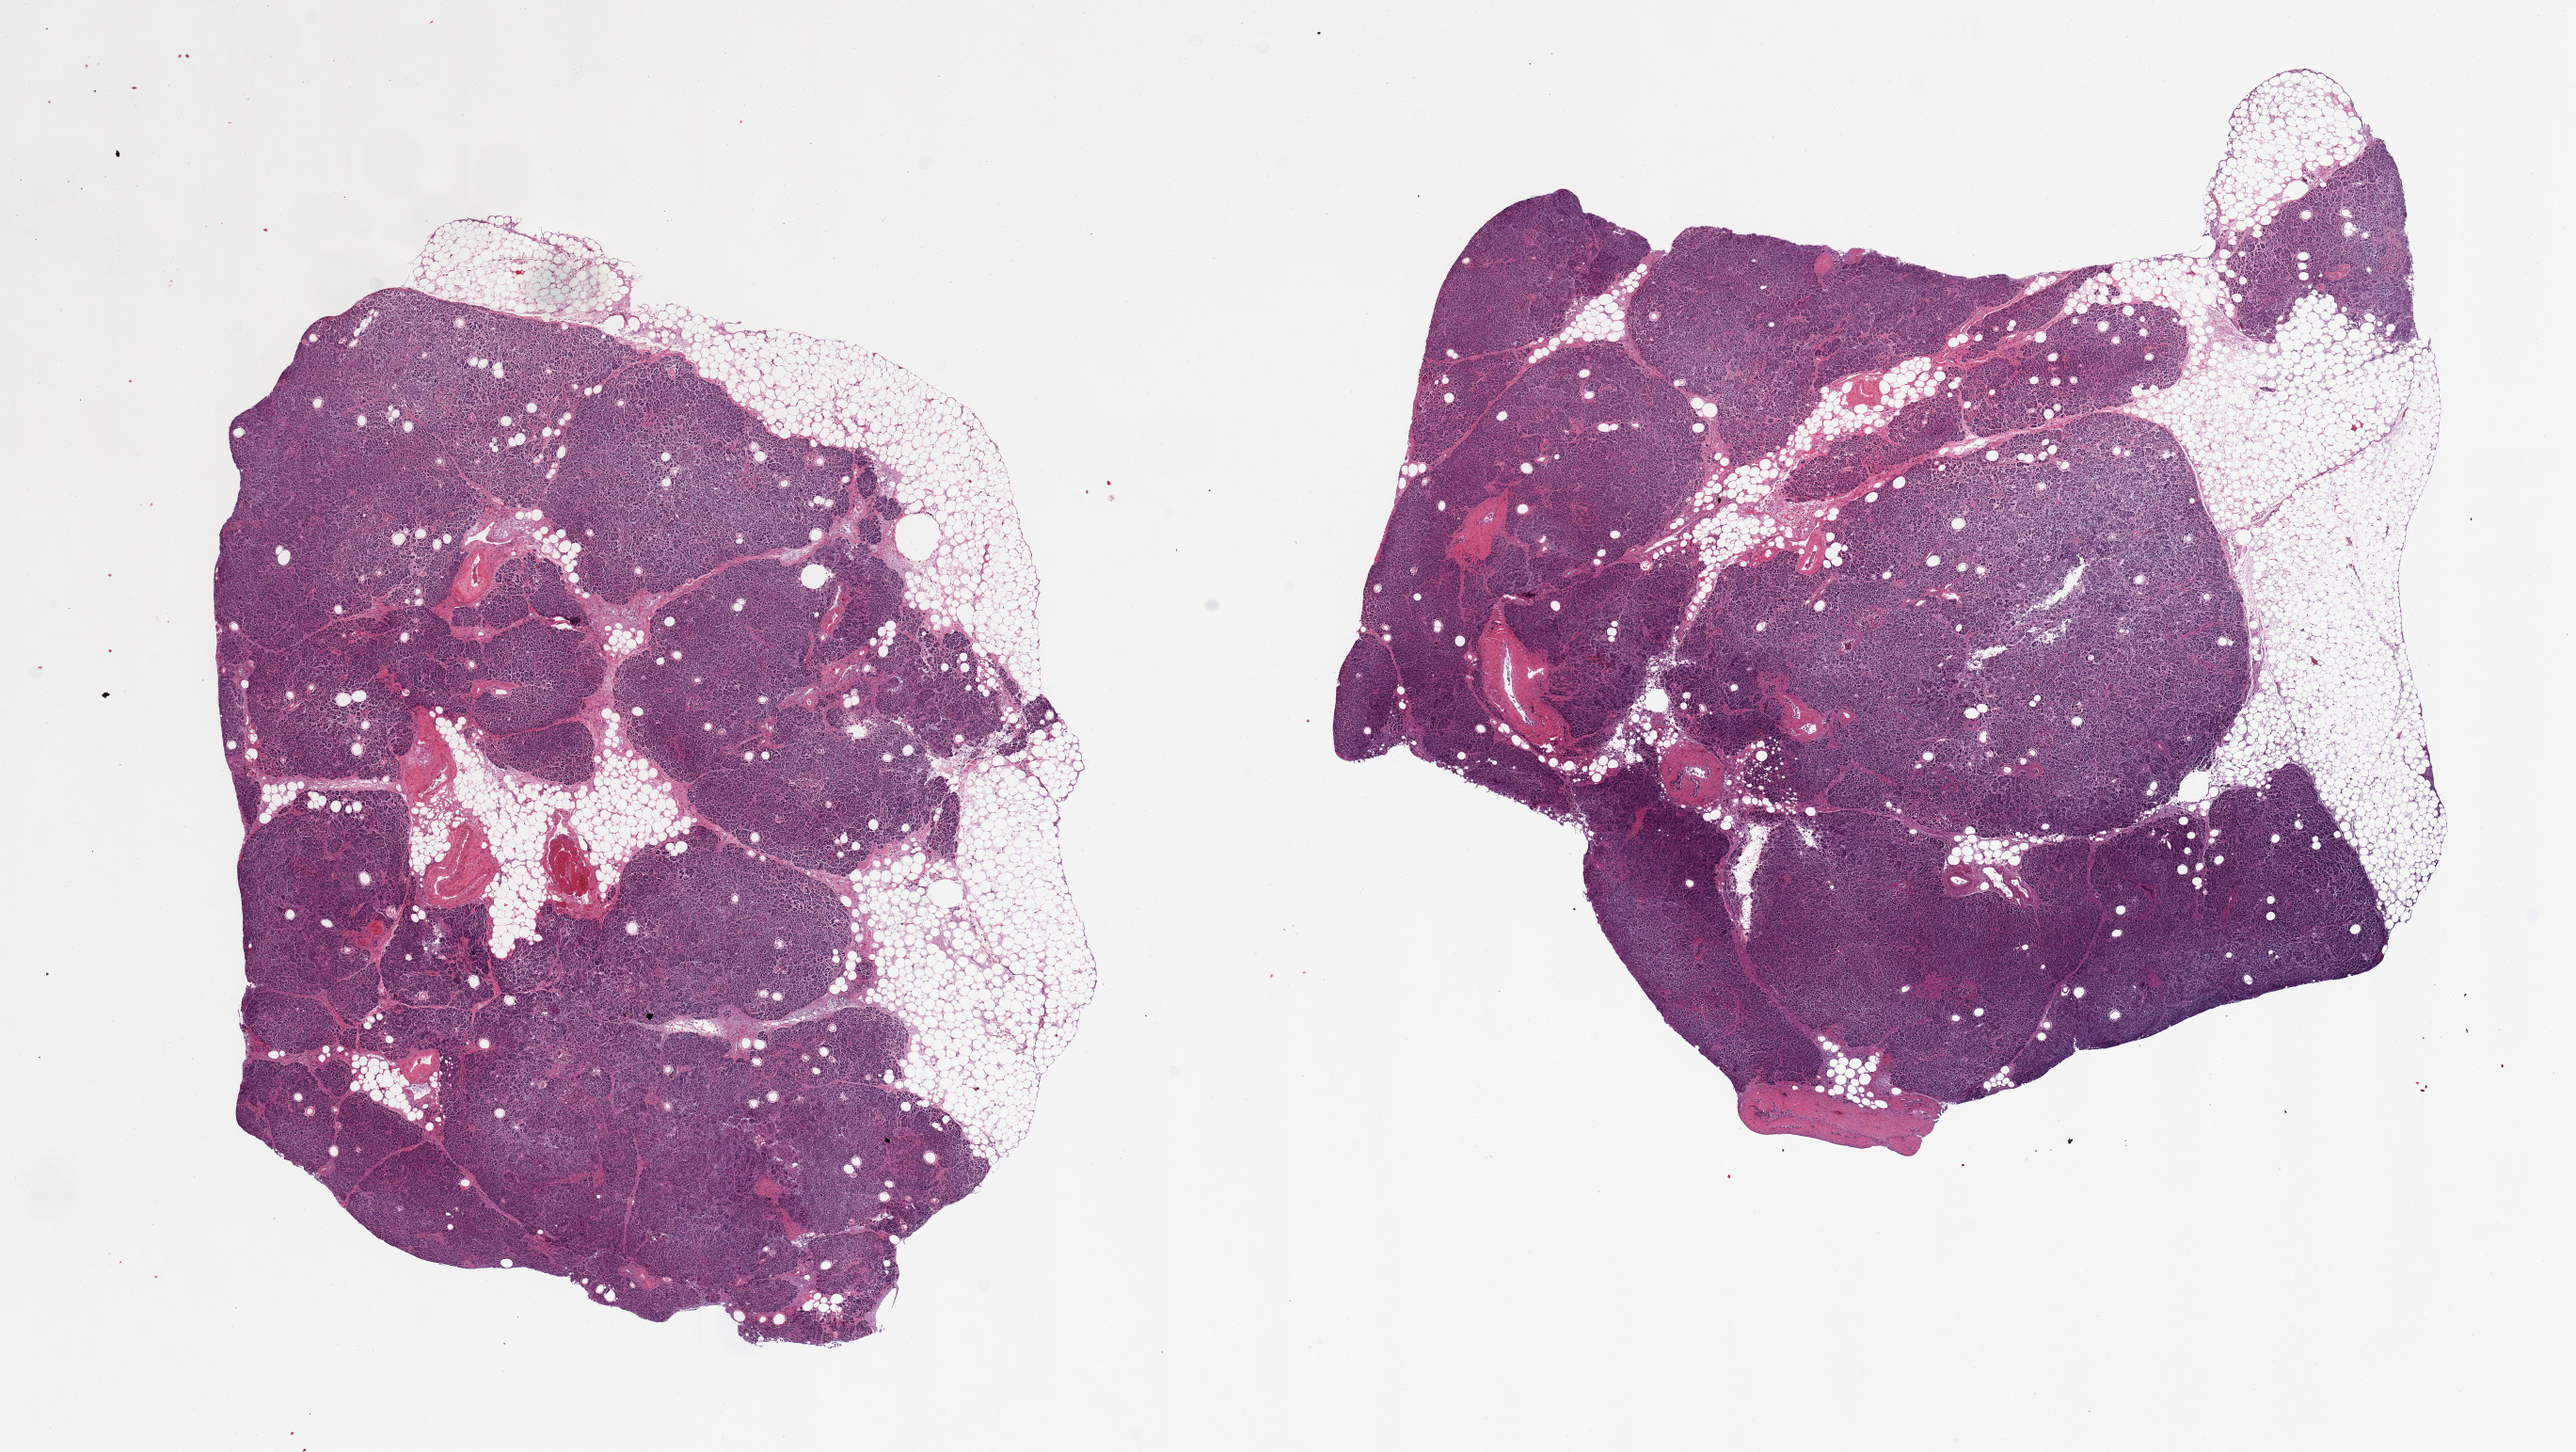
Digitized H&E-stained section, low-resolution overview of the scanned area, about 21.7 x 12.2 mm (slide scanned at 20x), PAXgene-fixed paraffin-embedded (PFPE) section, section of pancreas (target tissue), tissue donor sample. Donor: male.
Review note (as recorded): 2 pieces; 20% peripheral and internal fat.